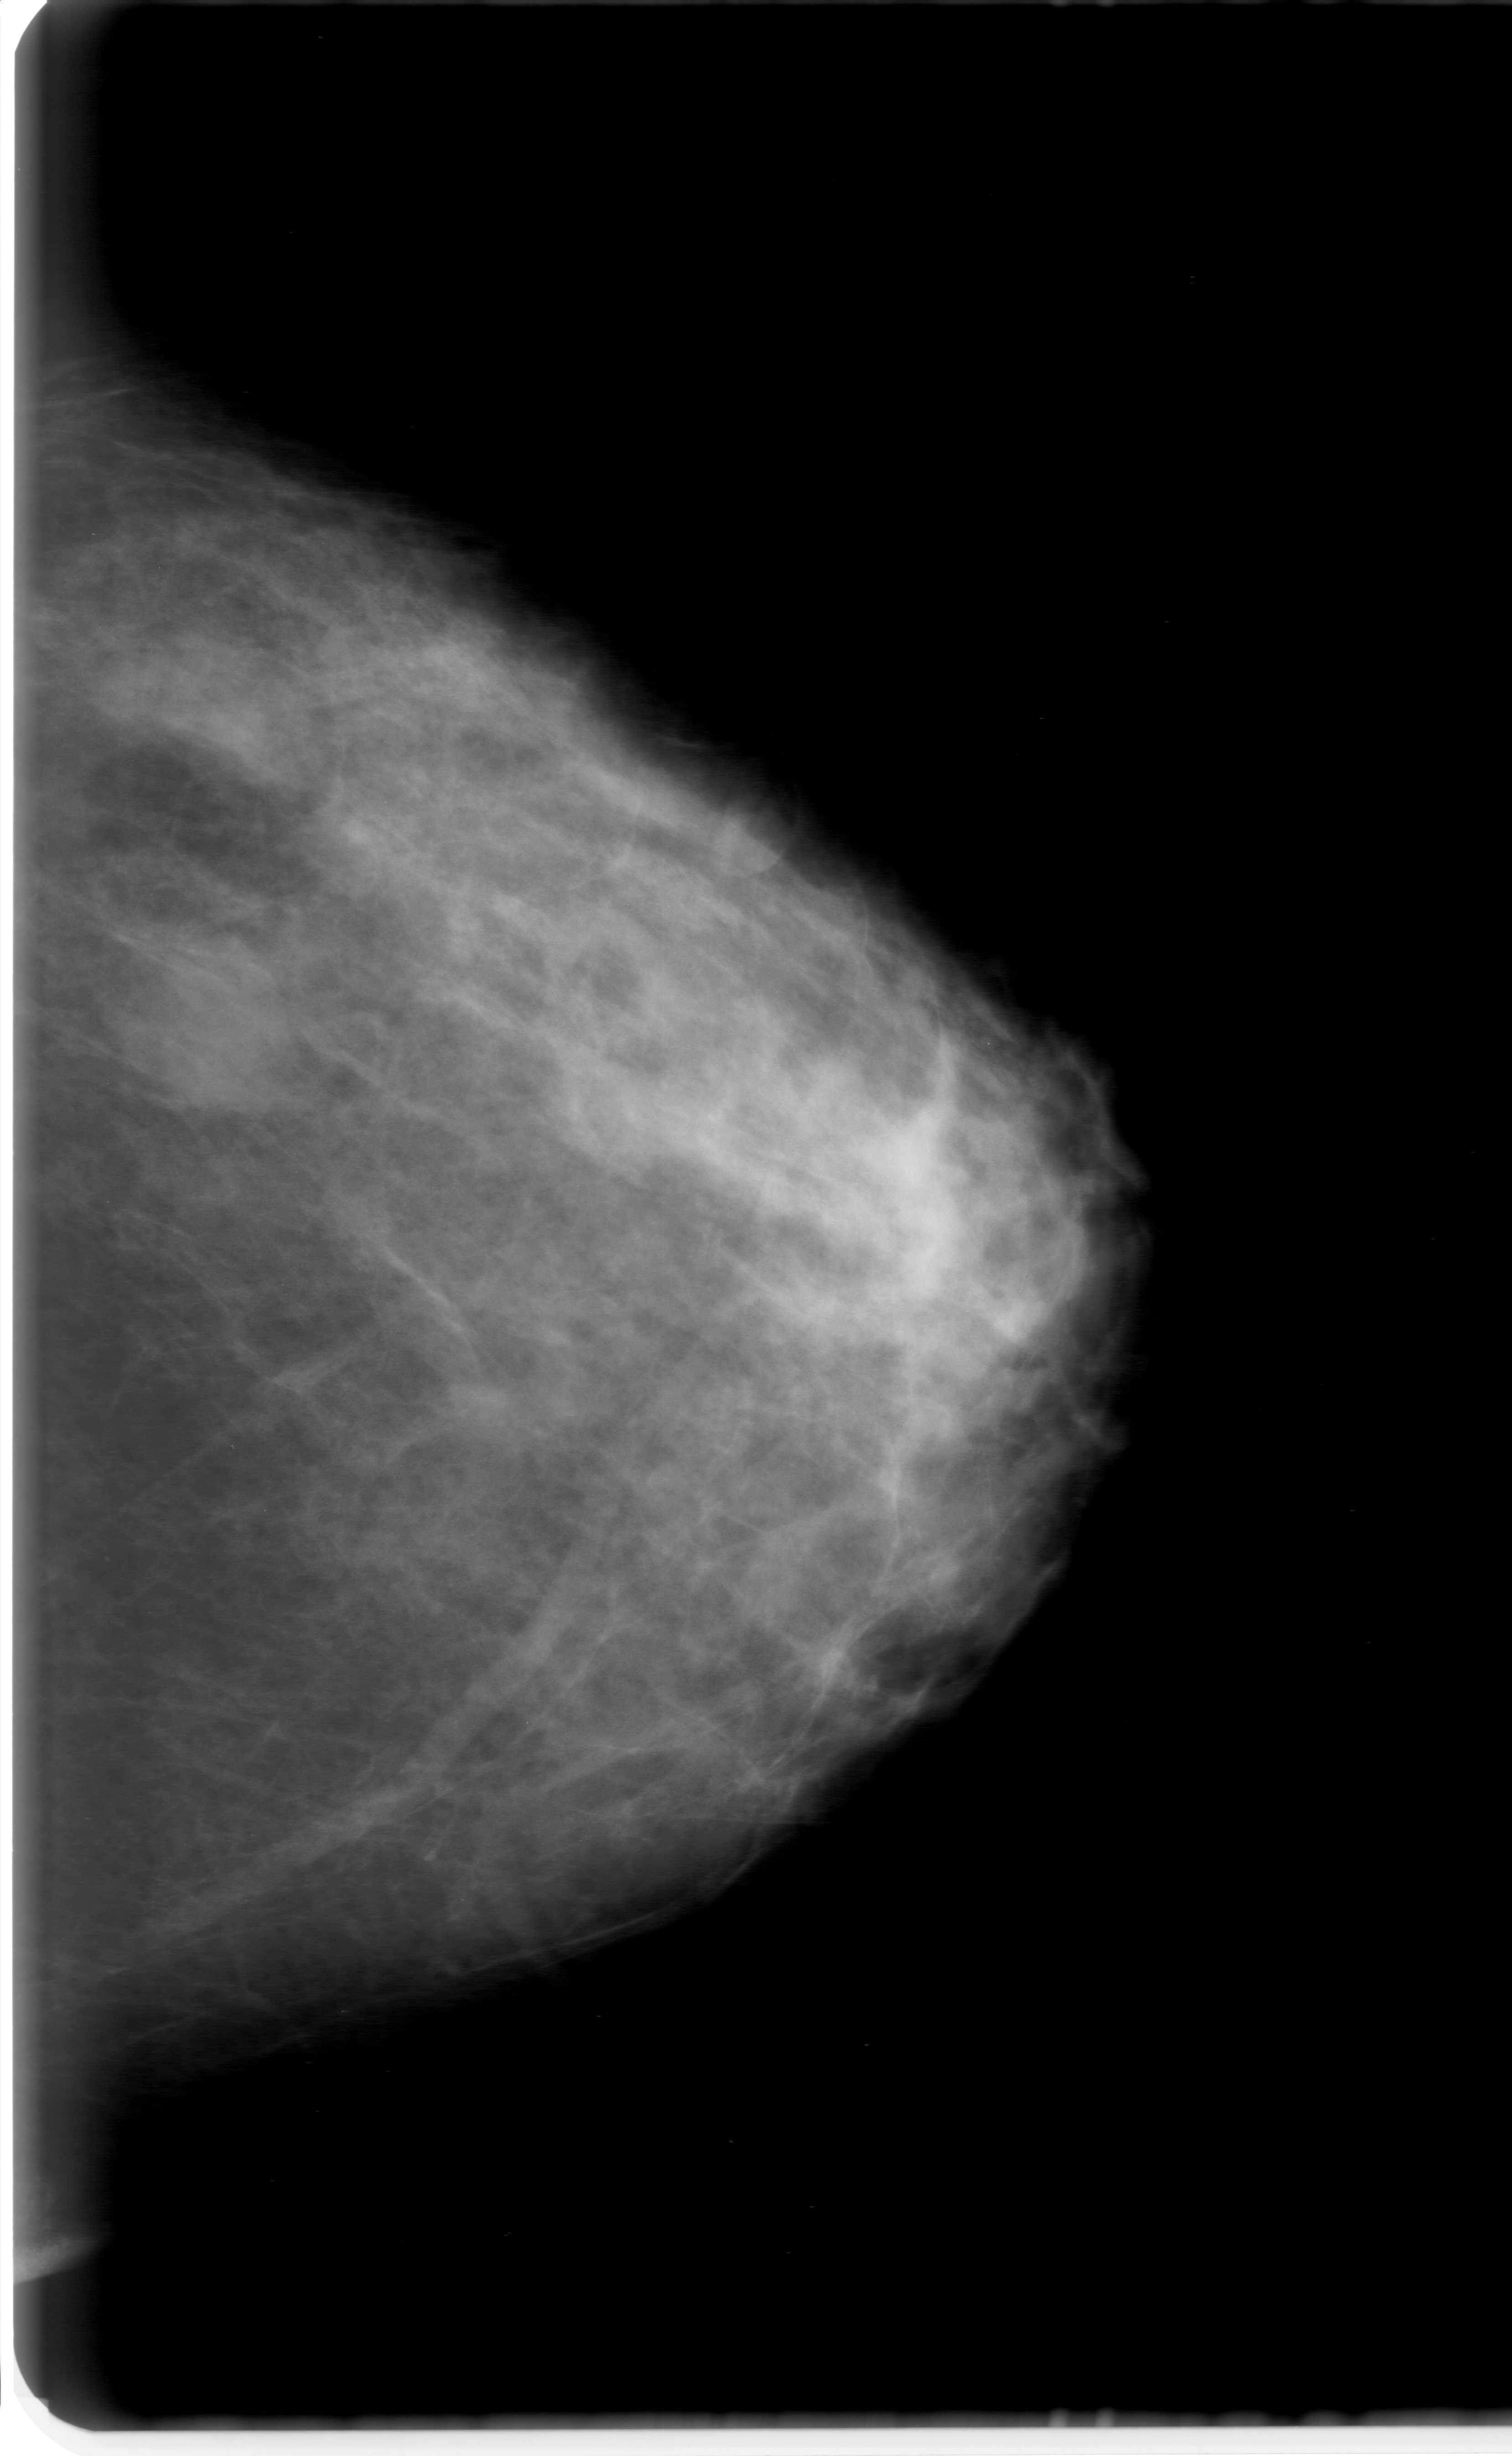
Mammogram (digitized film), left breast, CC view, BI-RADS breast density category 3 (scale 1–4).
Marked abnormality: mass, shape oval, margins obscured; BI-RADS assessment category 0 (incomplete: needs additional imaging); pathology (as recorded): benign.